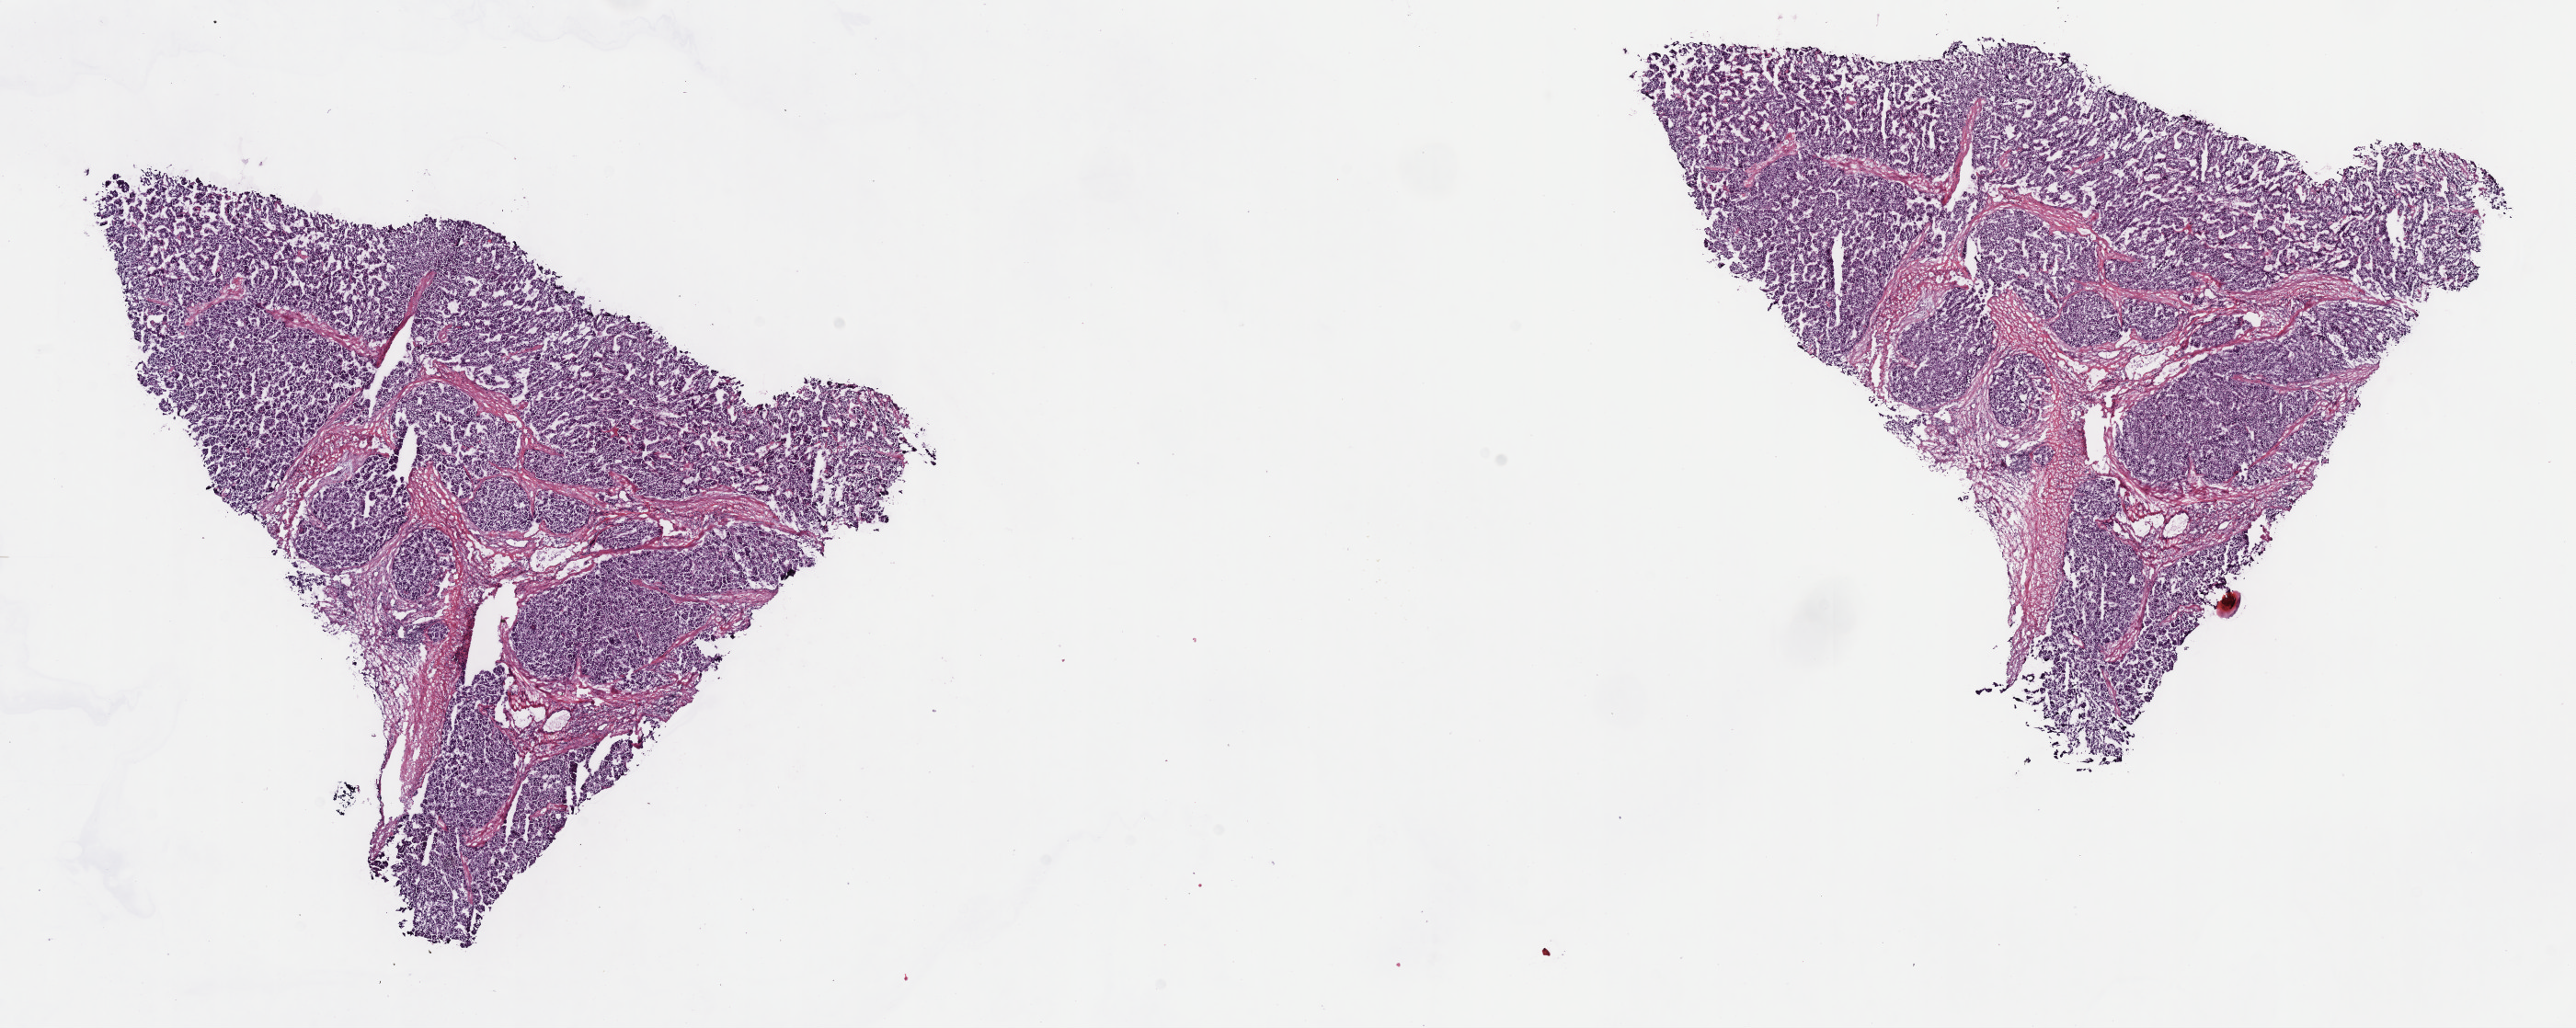
H&E whole-slide image, shown as a low-resolution overview of the whole scanned area (about 22.7 x 9.0 mm, acquisition: 40x scan), frozen section, sample: primary tumour, liver. Male, age 72 years at initial diagnosis. Histologic grade: G3 (poorly differentiated). Composition of this section per pathologist review: tumour cells 80%, tumour nuclei 80%, normal cells 0%, stromal cells 20%, necrosis 0%. Inflammatory infiltration, as recorded: lymphocyte infiltration 3%, monocyte infiltration 1%, neutrophil infiltration 3%.
* AJCC pathologic stage: I (6th edition)
* histologic diagnosis: Hepatocellular carcinoma, NOS